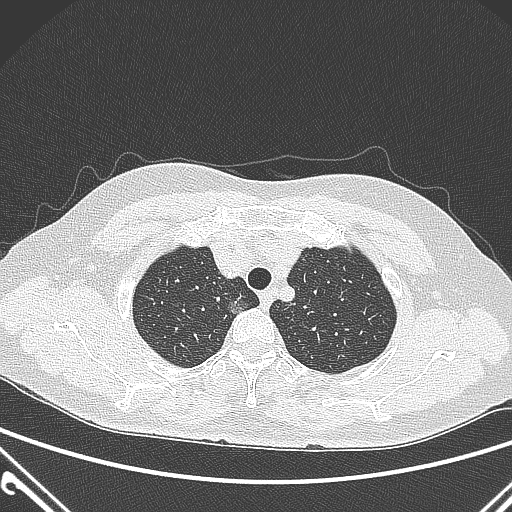
Chest CT, one axial slice. Slice 239 of 300 in the series (ordered by position). 120 kVp. Lung window (W 1500 / L -600 HU). 1 mm slice thickness. 512 × 512 image matrix, field of view 350 × 350 mm. Patient: female, 54 years. Case-level facts recorded for this patient, not image findings: clinical TNM (as recorded): T1a N0 M0; histopathological grade: G1.
Outlined on this slice (rectangle marked by the reading radiologist):
- lung tumour (recorded histology: adenocarcinoma): box from (x=223, y=295) to (x=255, y=325) px